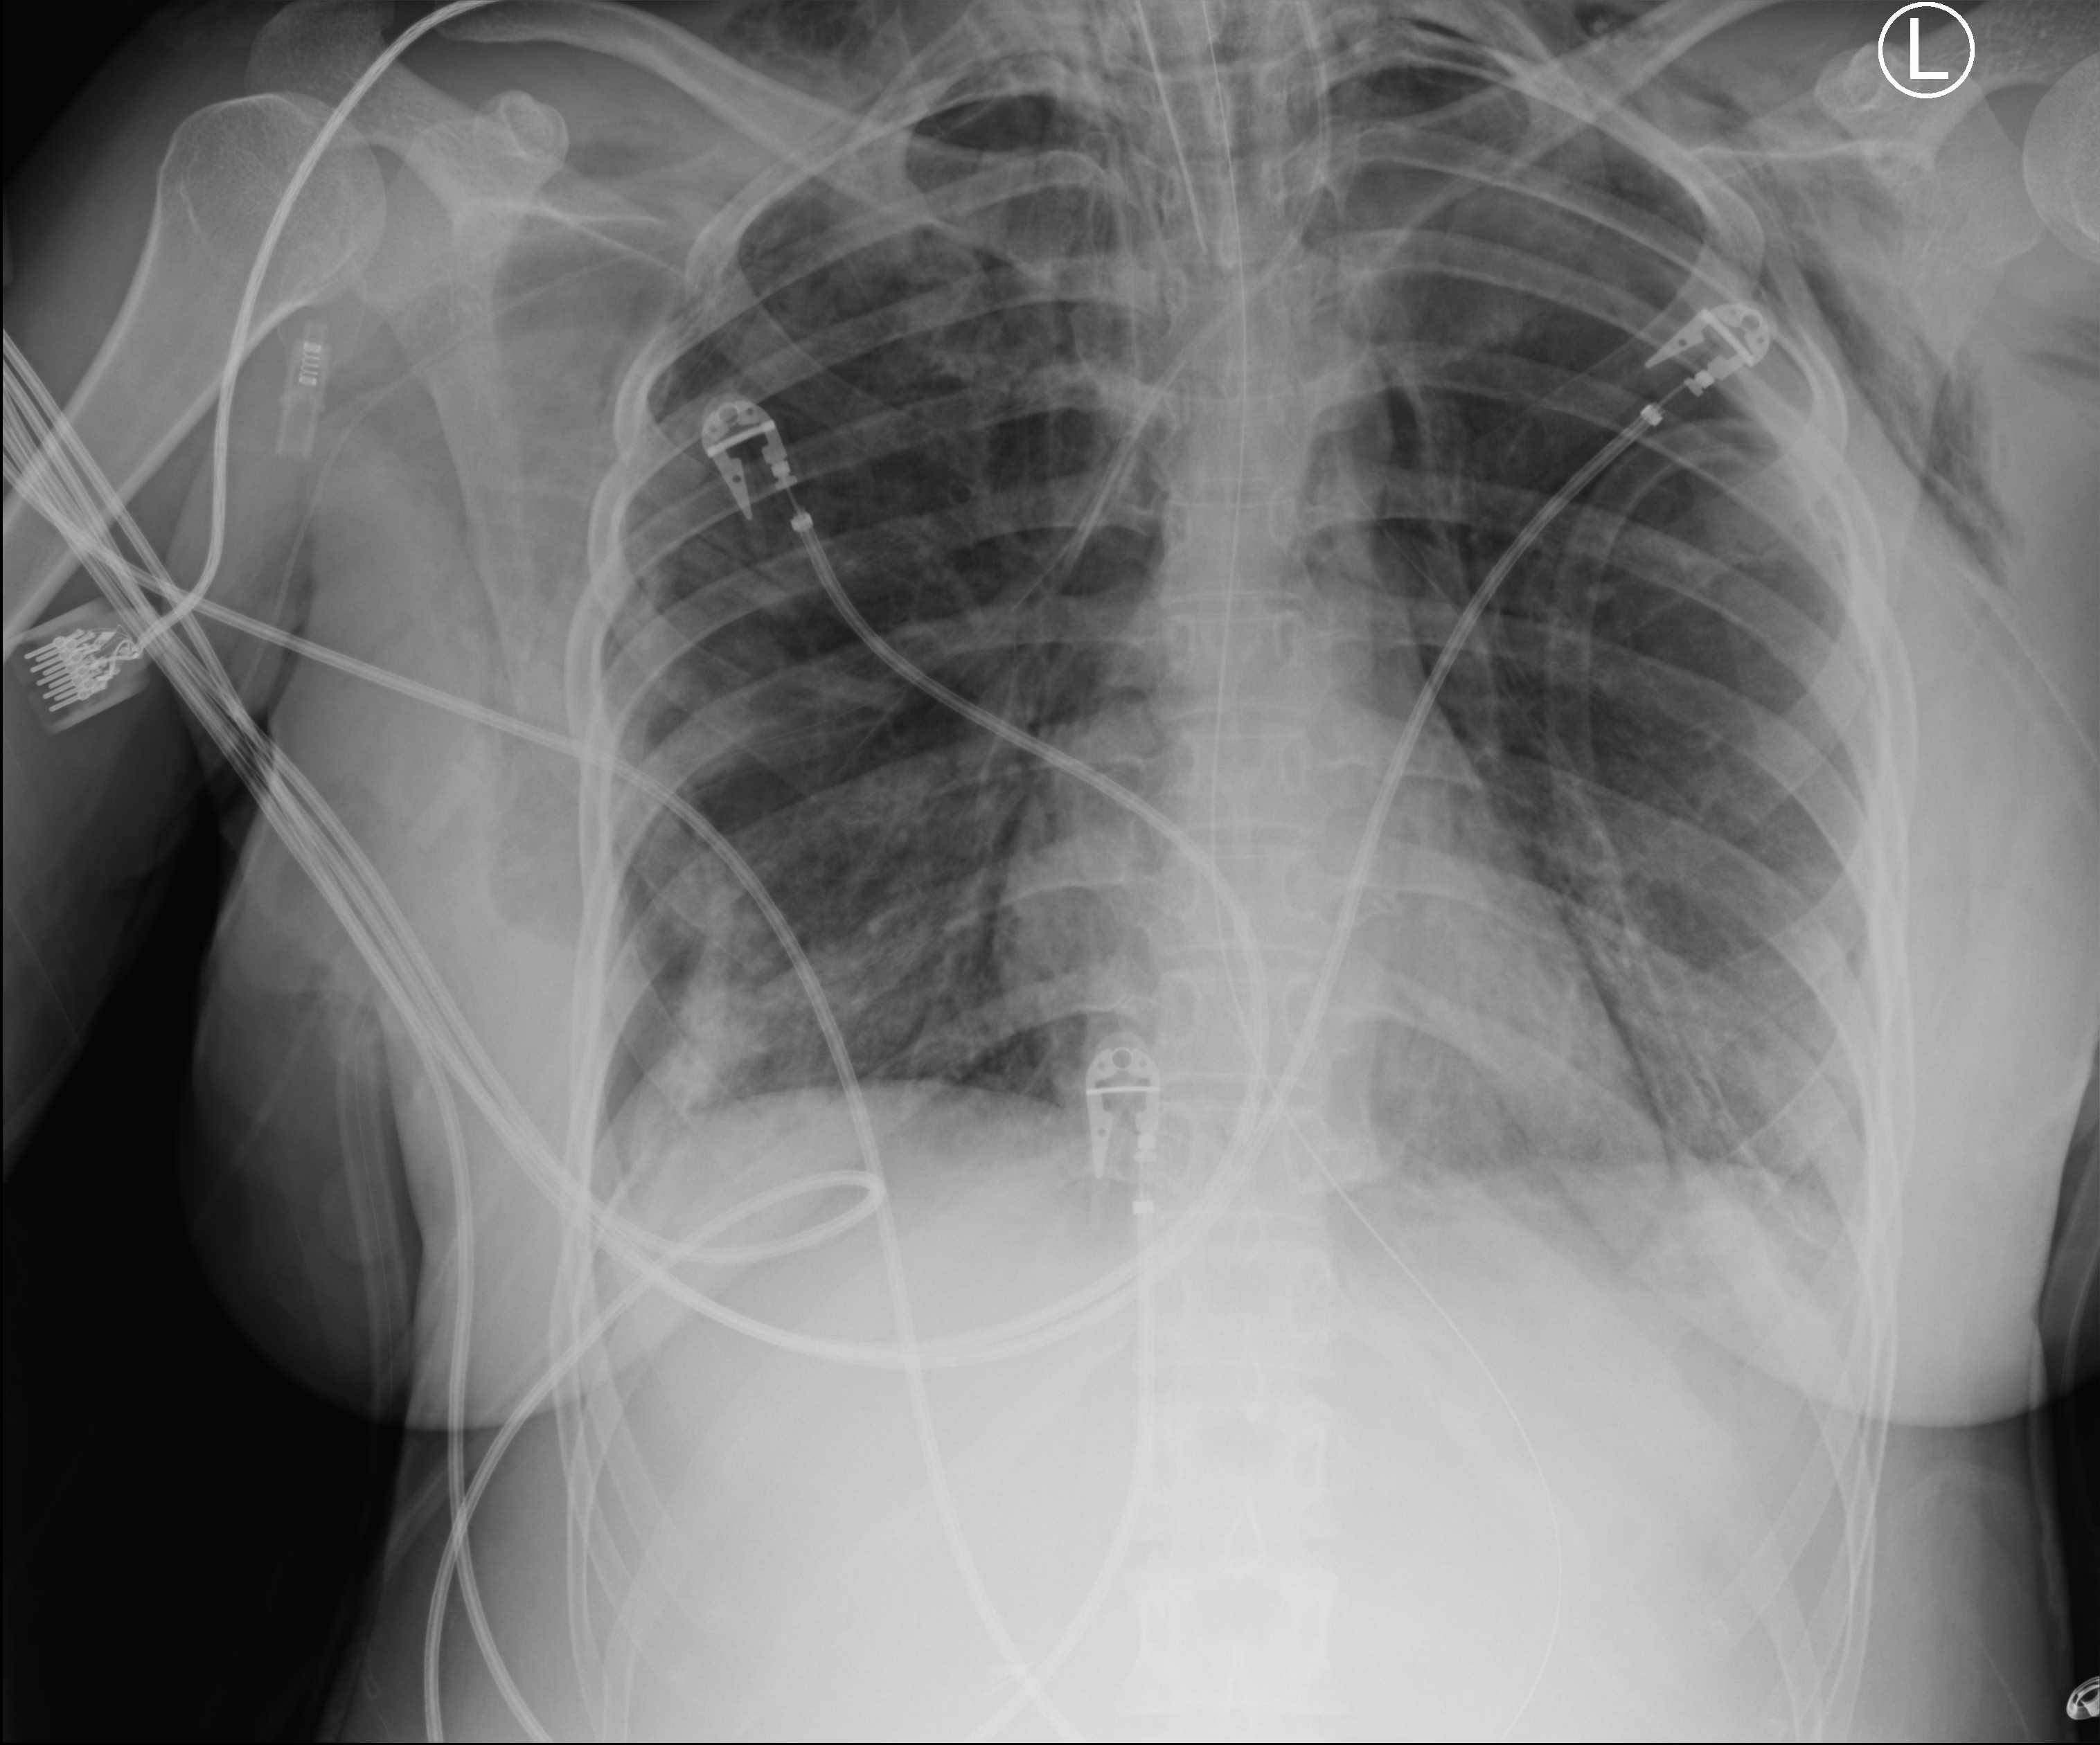
Bedside chest radiograph (computed radiography), anteroposterior (AP) projection. Patient hospitalised with COVID-19, aged 18–59 years.
Admission-level facts for this patient (not findings on this image; timing relative to this image not recorded):
- chronic kidney disease (admission record): no